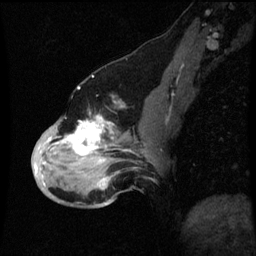
Breast MRI (dynamic contrast-enhanced), one sagittal slice; position 26 of 60 along the scan axis; dynamic contrast-enhanced series, image 2 of 3 at this slice position (ordered by acquisition); 1.5 T; TE 4.2 ms, TR 8.9 ms; 2 mm slice thickness; 256 × 256 image matrix. Patient: female, 49 years. From the clinical record (not read from this slice): setting: breast cancer imaged before/during neoadjuvant chemotherapy; receptor status: HR-positive, HER2-negative.
Outlined on this slice (semi-automatic segmentation, software-assisted and operator-edited):
- analysis volume of interest (the breast-tissue region the enhancement analysis was run in; not a lesion): bounding box <32,100,151,199> (left, top, right, bottom; pixels)
- tumour enhancement mask (voxels above the 70 % enhancement threshold inside the analysis volume of interest): <34,106,123,185>